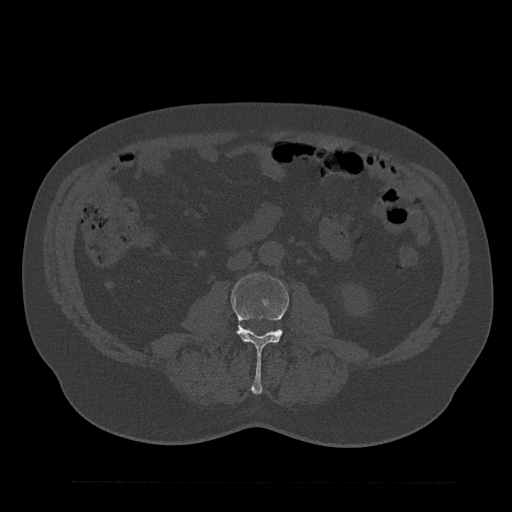
CT including the spine, one axial slice; reconstruction kernel Br40s/3; bone window (W 1800 / L 400 HU); 0.5 mm slice thickness; 512 × 512 image matrix, field of view 430 × 430 mm. Patient: male, 61 years. From the clinical record (not read from this slice): primary cancer: prostate.
Annotated regions visible in this slice (semi-automatic segmentation, software-assisted and operator-edited):
- L3 vertebra: bounding box [x1, y1, x2, y2] px = [231, 273, 289, 394]